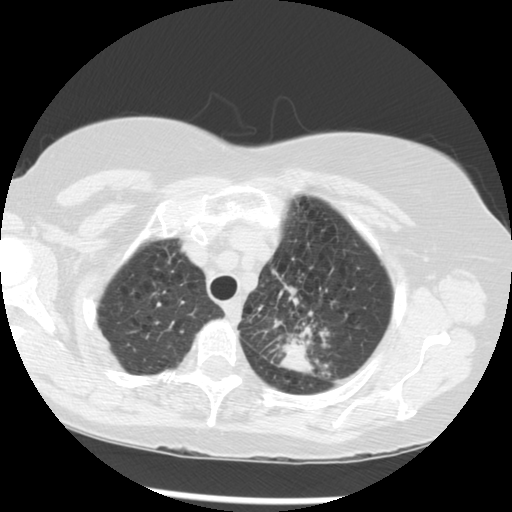
Chest CT (low-dose screening protocol), one axial image, third screening round (two years after baseline), lung window (W 1500 / L -600 HU), standard (soft-tissue) reconstruction kernel (STANDARD), slice 235 of 283 in the series, 512 × 512 image matrix. Female participant, aged 70 years at enrolment. Current smoker at enrolment.
Lesion marked by an expert reader, bounding box <252,285,349,373> (left, top, right, bottom; pixels). Reader record for this screening exam (exam-level; its link to the box is not recorded): non-calcified nodule or mass ≥4 mm, left upper lobe, 32 × 26 mm, spiculated (stellate) margins, soft tissue attenuation, pre-existing on the prior screen: yes; interval growth: yes.